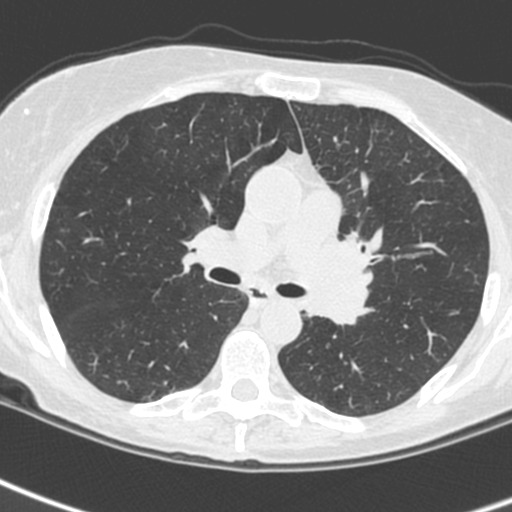
Low-dose screening chest CT, one axial slice. Lung window (W 1500 / L -600 HU). 1.3 mm slice thickness. 512 × 512 image matrix, field of view 284 × 284 mm.
Annotated regions visible in this slice (expert manual segmentation):
- lesion 3 (tumor, upper lobe of left lung): bounding box [x1, y1, x2, y2] px = [305, 237, 373, 326]